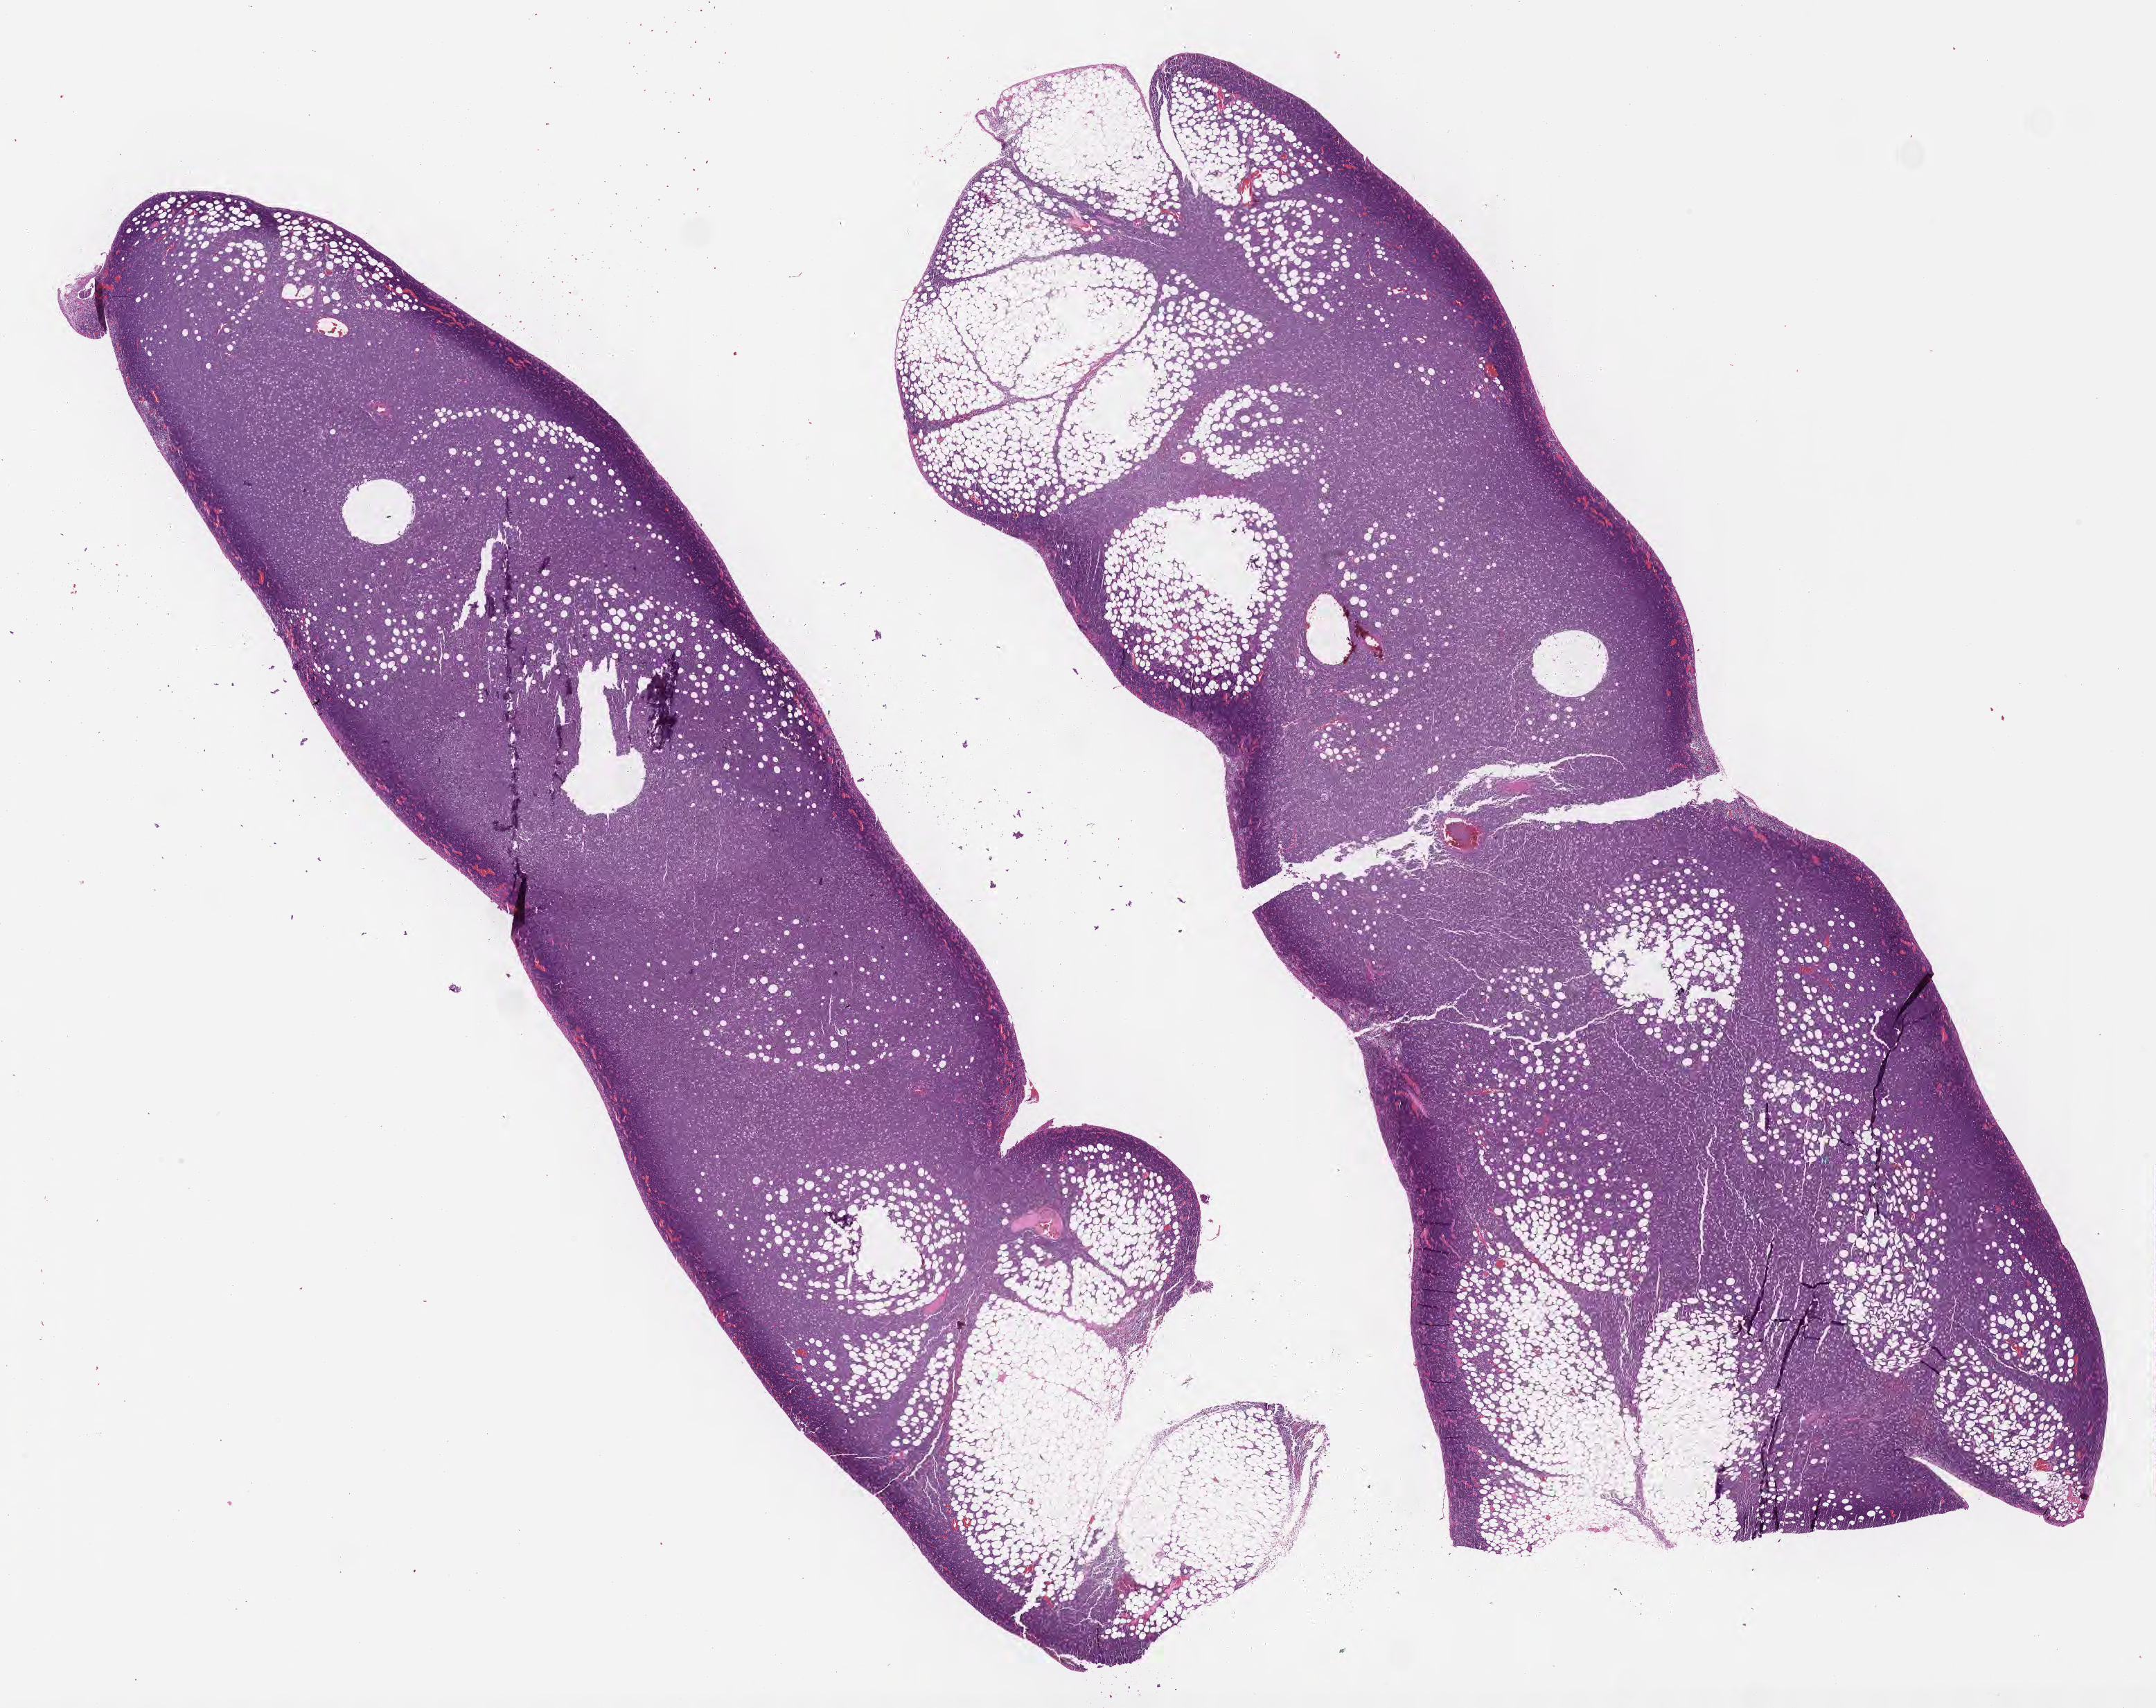
H&E whole-slide image — low-resolution overview of the scanned area, about 25.2 x 19.9 mm; formalin-fixed paraffin-embedded section; primary tumor. Patient male; 32 years old. Composition of this section per pathologist review: tumor cells 80%, tumor nuclei 95%, stromal cells 5%, necrosis 5%, normal cells 10%. Infiltration values recorded for this section: lymphocyte infiltration 40%, monocyte infiltration 30%, neutrophil infiltration 5%.
Diagnosis: Burkitt lymphoma, NOS. Section: bottom of the tissue portion. Ann Arbor stage (patient): Stage IV.